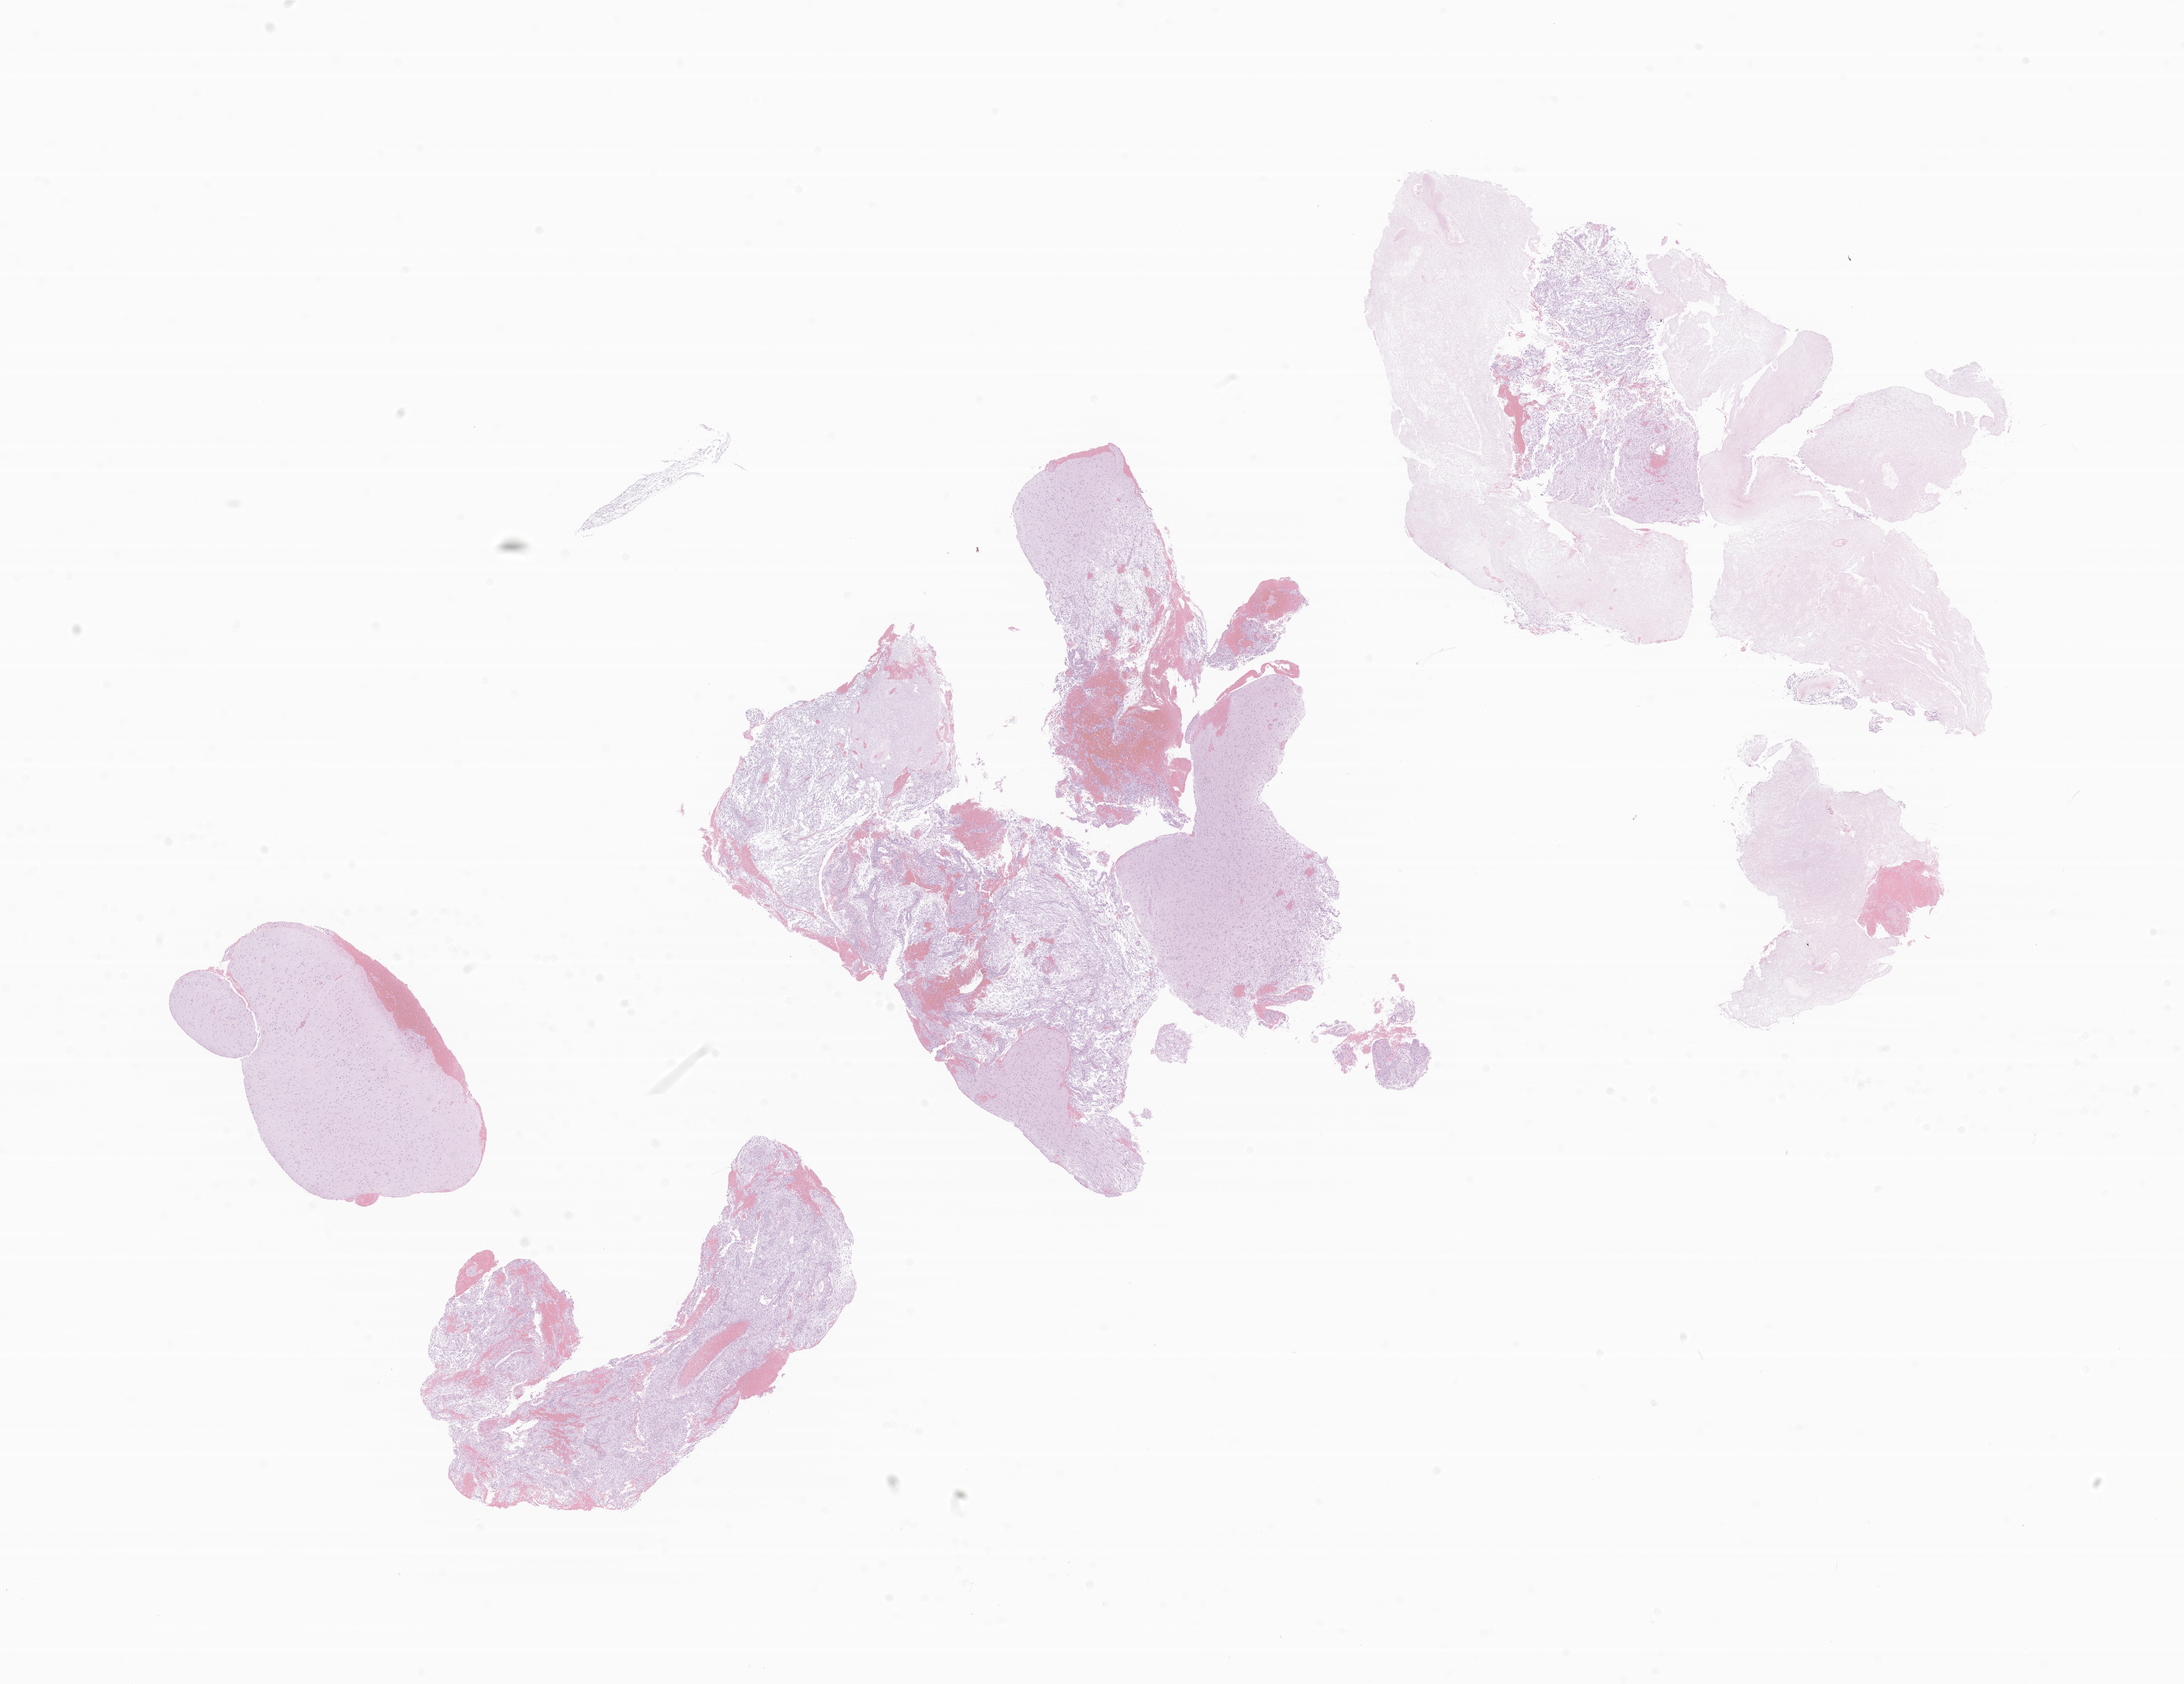
Whole-slide image, H&E stain of tumor tissue from the temporal lobe, shown as a low-resolution overview of the whole scanned area (about 23.7 x 18.3 mm), formalin-fixed, paraffin-embedded (FFPE) tissue. Female patient, age 135 months (11 years 3 months).
Diagnosis (ICD-O-3 morphology term): Ganglioglioma, NOS.